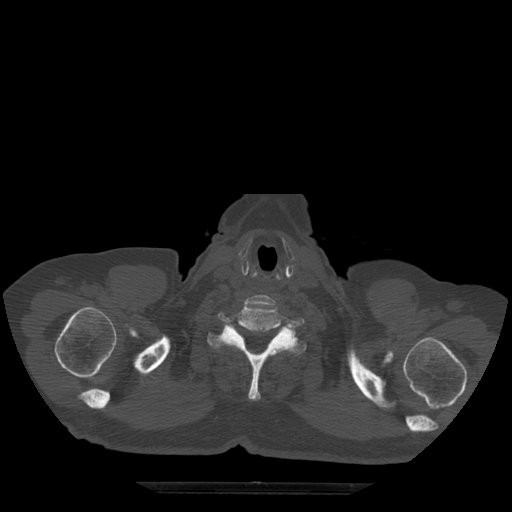
CT including the spine, one axial slice. Position 448 of 522 along the scan axis. Bone window (W 1800 / L 400 HU). 1.25 mm slice thickness. 512 × 512 image matrix, field of view 420 × 420 mm. Patient age 72 years. Case-level facts recorded for this patient, not image findings: primary cancer: prostate.
Annotated regions visible in this slice (semi-automatically segmented with operator editing):
- T1 vertebra: bounding box [x1, y1, x2, y2] px = [207, 326, 307, 401]